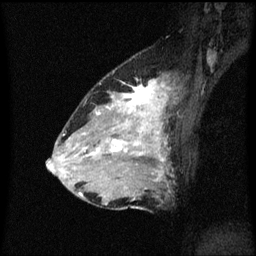
Breast MRI (dynamic contrast-enhanced), one sagittal slice; slice 37 of 60 in the series (ordered by position); dynamic contrast-enhanced series, image 2 of 3 at this slice position (ordered by acquisition); 1.5 T; TE 4.2 ms, TR 8.4 ms; 2 mm slice thickness; 256 × 256 image matrix, field of view 200 × 200 mm. Female patient, age 34 years. From the clinical record (not read from this slice): setting: breast cancer imaged before/during neoadjuvant chemotherapy; receptor status: HR-positive, HER2-negative.
Structures marked on this image (semi-automatic segmentation, software-assisted and operator-edited):
- analysis volume of interest (the breast-tissue region the enhancement analysis was run in; not a lesion): bounding box [x1, y1, x2, y2] px = [69, 70, 176, 209]
- tumour enhancement mask (voxels above the 70 % enhancement threshold inside the analysis volume of interest): [79, 80, 168, 195]